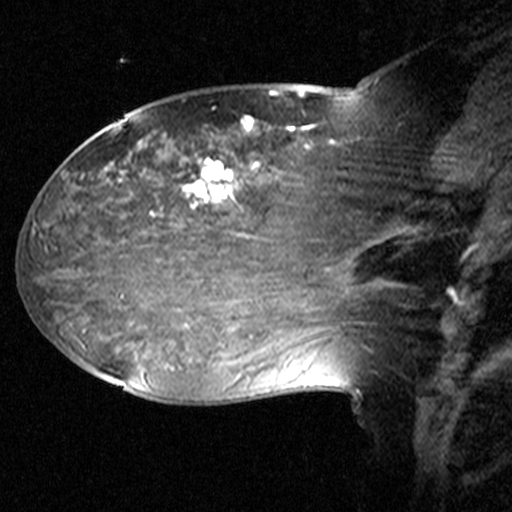
Breast MRI (dynamic contrast-enhanced), one sagittal slice. Position 22 of 44 along the scan axis. Dynamic contrast-enhanced study with each time point stored as its own series, time point 2 of 3 at this slice position (early post-contrast, ordered by acquisition time). 1.5 T. TE 4.5 ms, TR 11 ms. 3 mm slice thickness. 512 × 512 image matrix, field of view 240 × 240 mm. Patient: female, 38 years. From the clinical record (not read from this slice): setting: breast cancer imaged before/during neoadjuvant chemotherapy; receptor status: HR-positive, HER2-negative.
Structures marked on this image (semi-automatically segmented with operator editing):
- analysis volume of interest (the breast-tissue region the enhancement analysis was run in; not a lesion): bounding box [x1, y1, x2, y2] px = [124, 106, 405, 245]
- tumour enhancement mask (voxels above the 90 % enhancement threshold inside the analysis volume of interest): [183, 117, 309, 209]